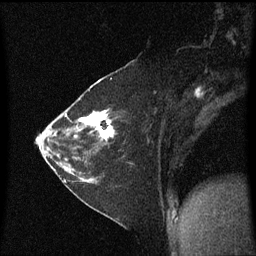
Breast MRI (dynamic contrast-enhanced), one sagittal slice. Position 32 of 60 along the scan axis. Dynamic contrast-enhanced series, image 2 of 3 at this slice position (ordered by acquisition). 1.5 T. TE 4.2 ms, TR 8.4 ms. 256 × 256 image matrix, field of view 200 × 200 mm. Female patient, age 36 years. From the clinical record (not read from this slice): setting: breast cancer imaged before/during neoadjuvant chemotherapy; receptor status: HR-positive, HER2-negative.
Outlined on this slice (semi-automatically segmented with operator editing):
- analysis volume of interest (the breast-tissue region the enhancement analysis was run in; not a lesion): bounding box [x1, y1, x2, y2] px = [66, 102, 124, 179]
- tumour enhancement mask (voxels above the 70 % enhancement threshold inside the analysis volume of interest): [66, 110, 116, 141]